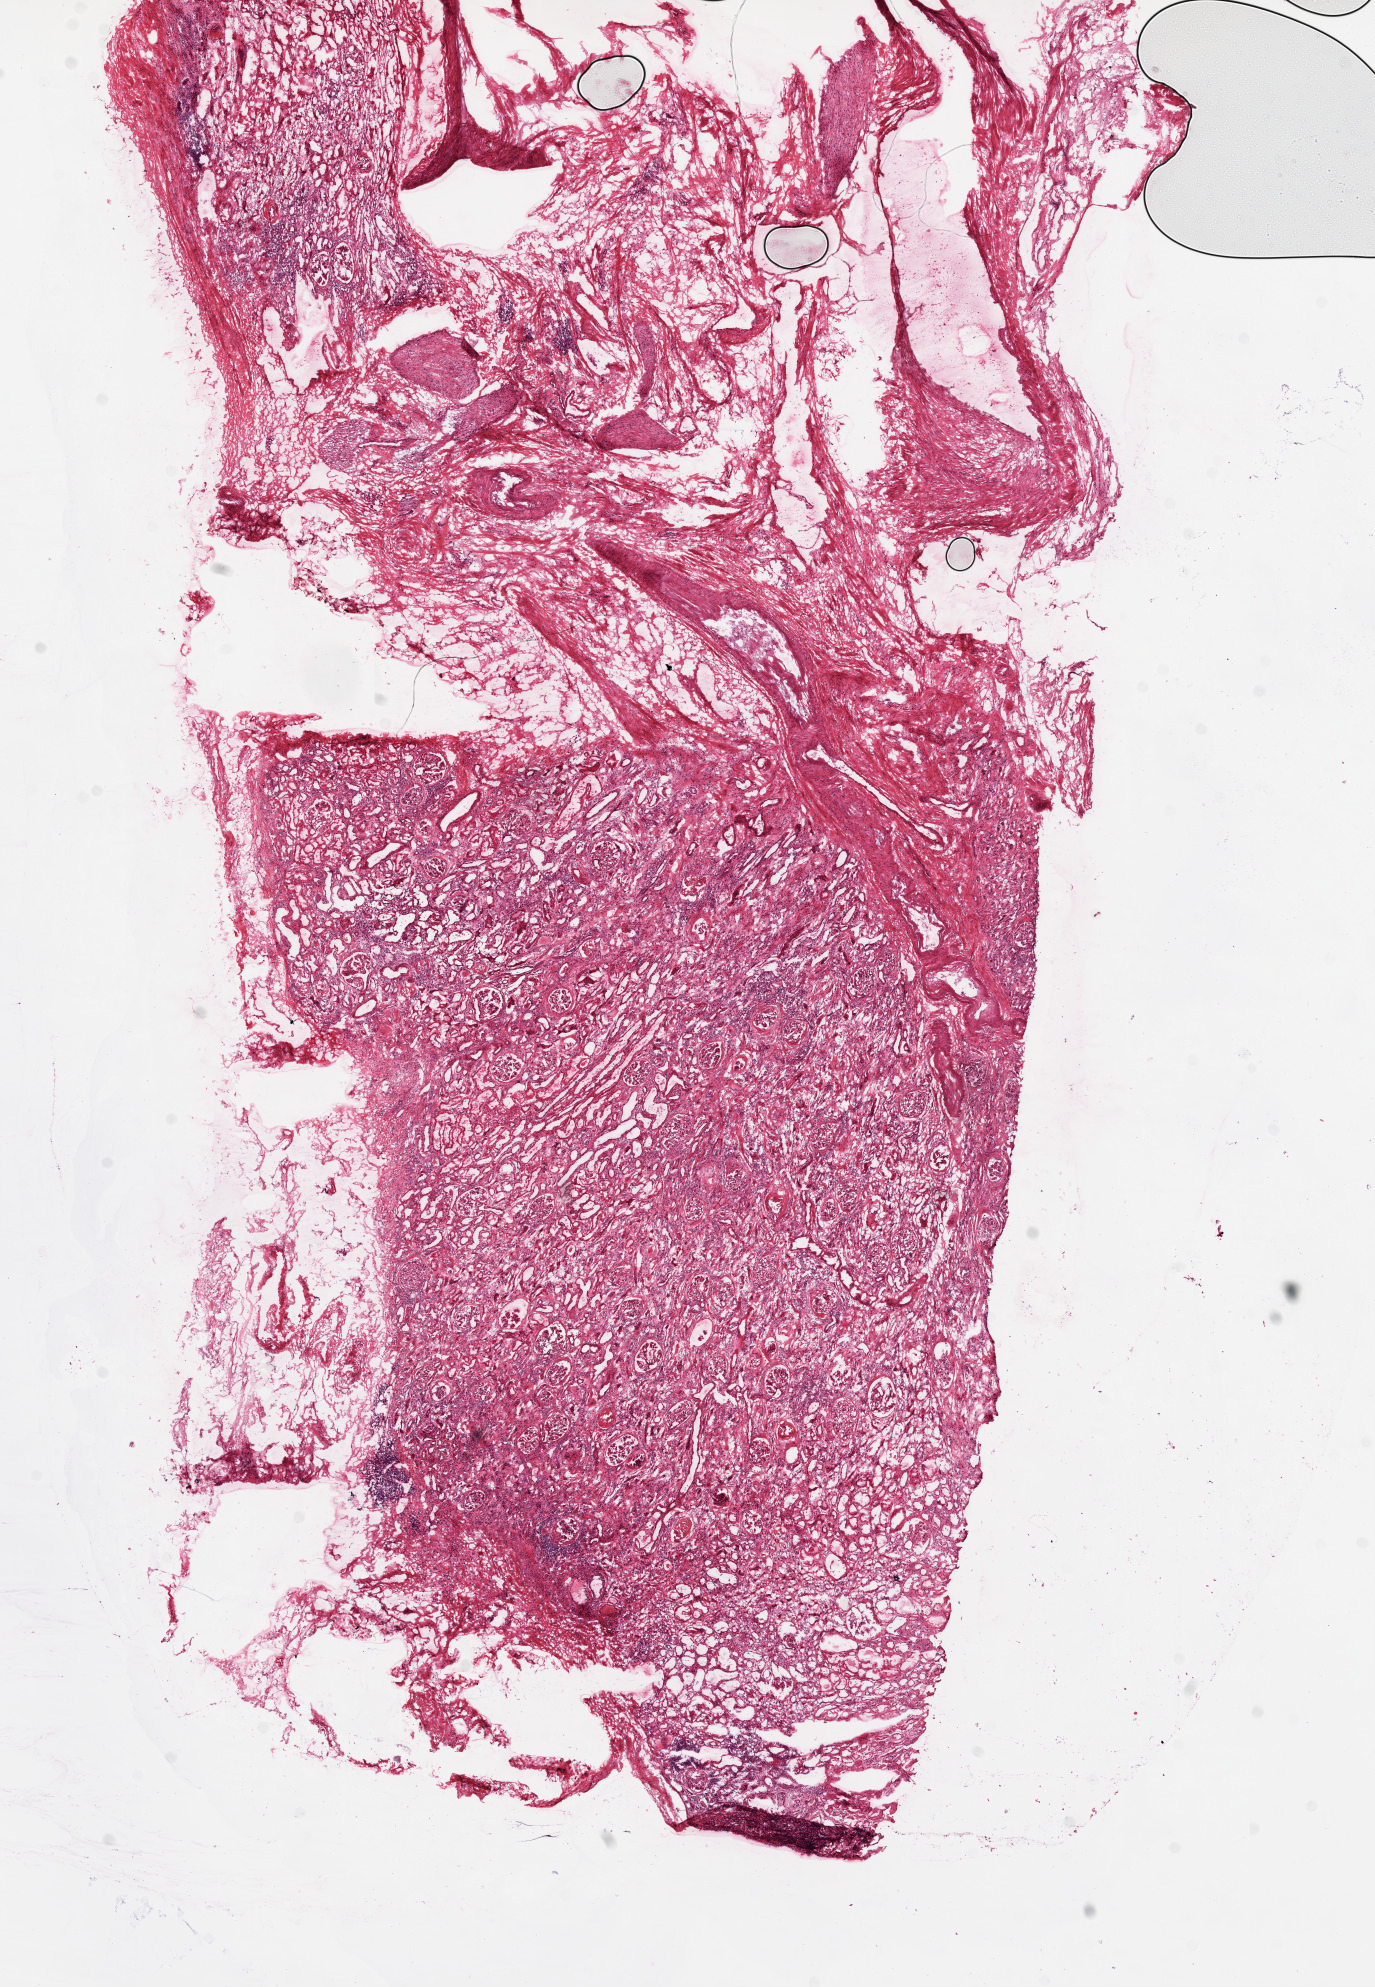
H&E whole-slide image, shown as a low-resolution overview of the whole scanned area (about 11.0 x 15.9 mm); frozen section from the top of the tissue portion; sample: solid tissue normal (non-tumour tissue), kidney. Female, age 68 years at initial diagnosis.
This section: solid tissue normal sample (biorepository sample class). Patient diagnosis: Clear cell adenocarcinoma, NOS.